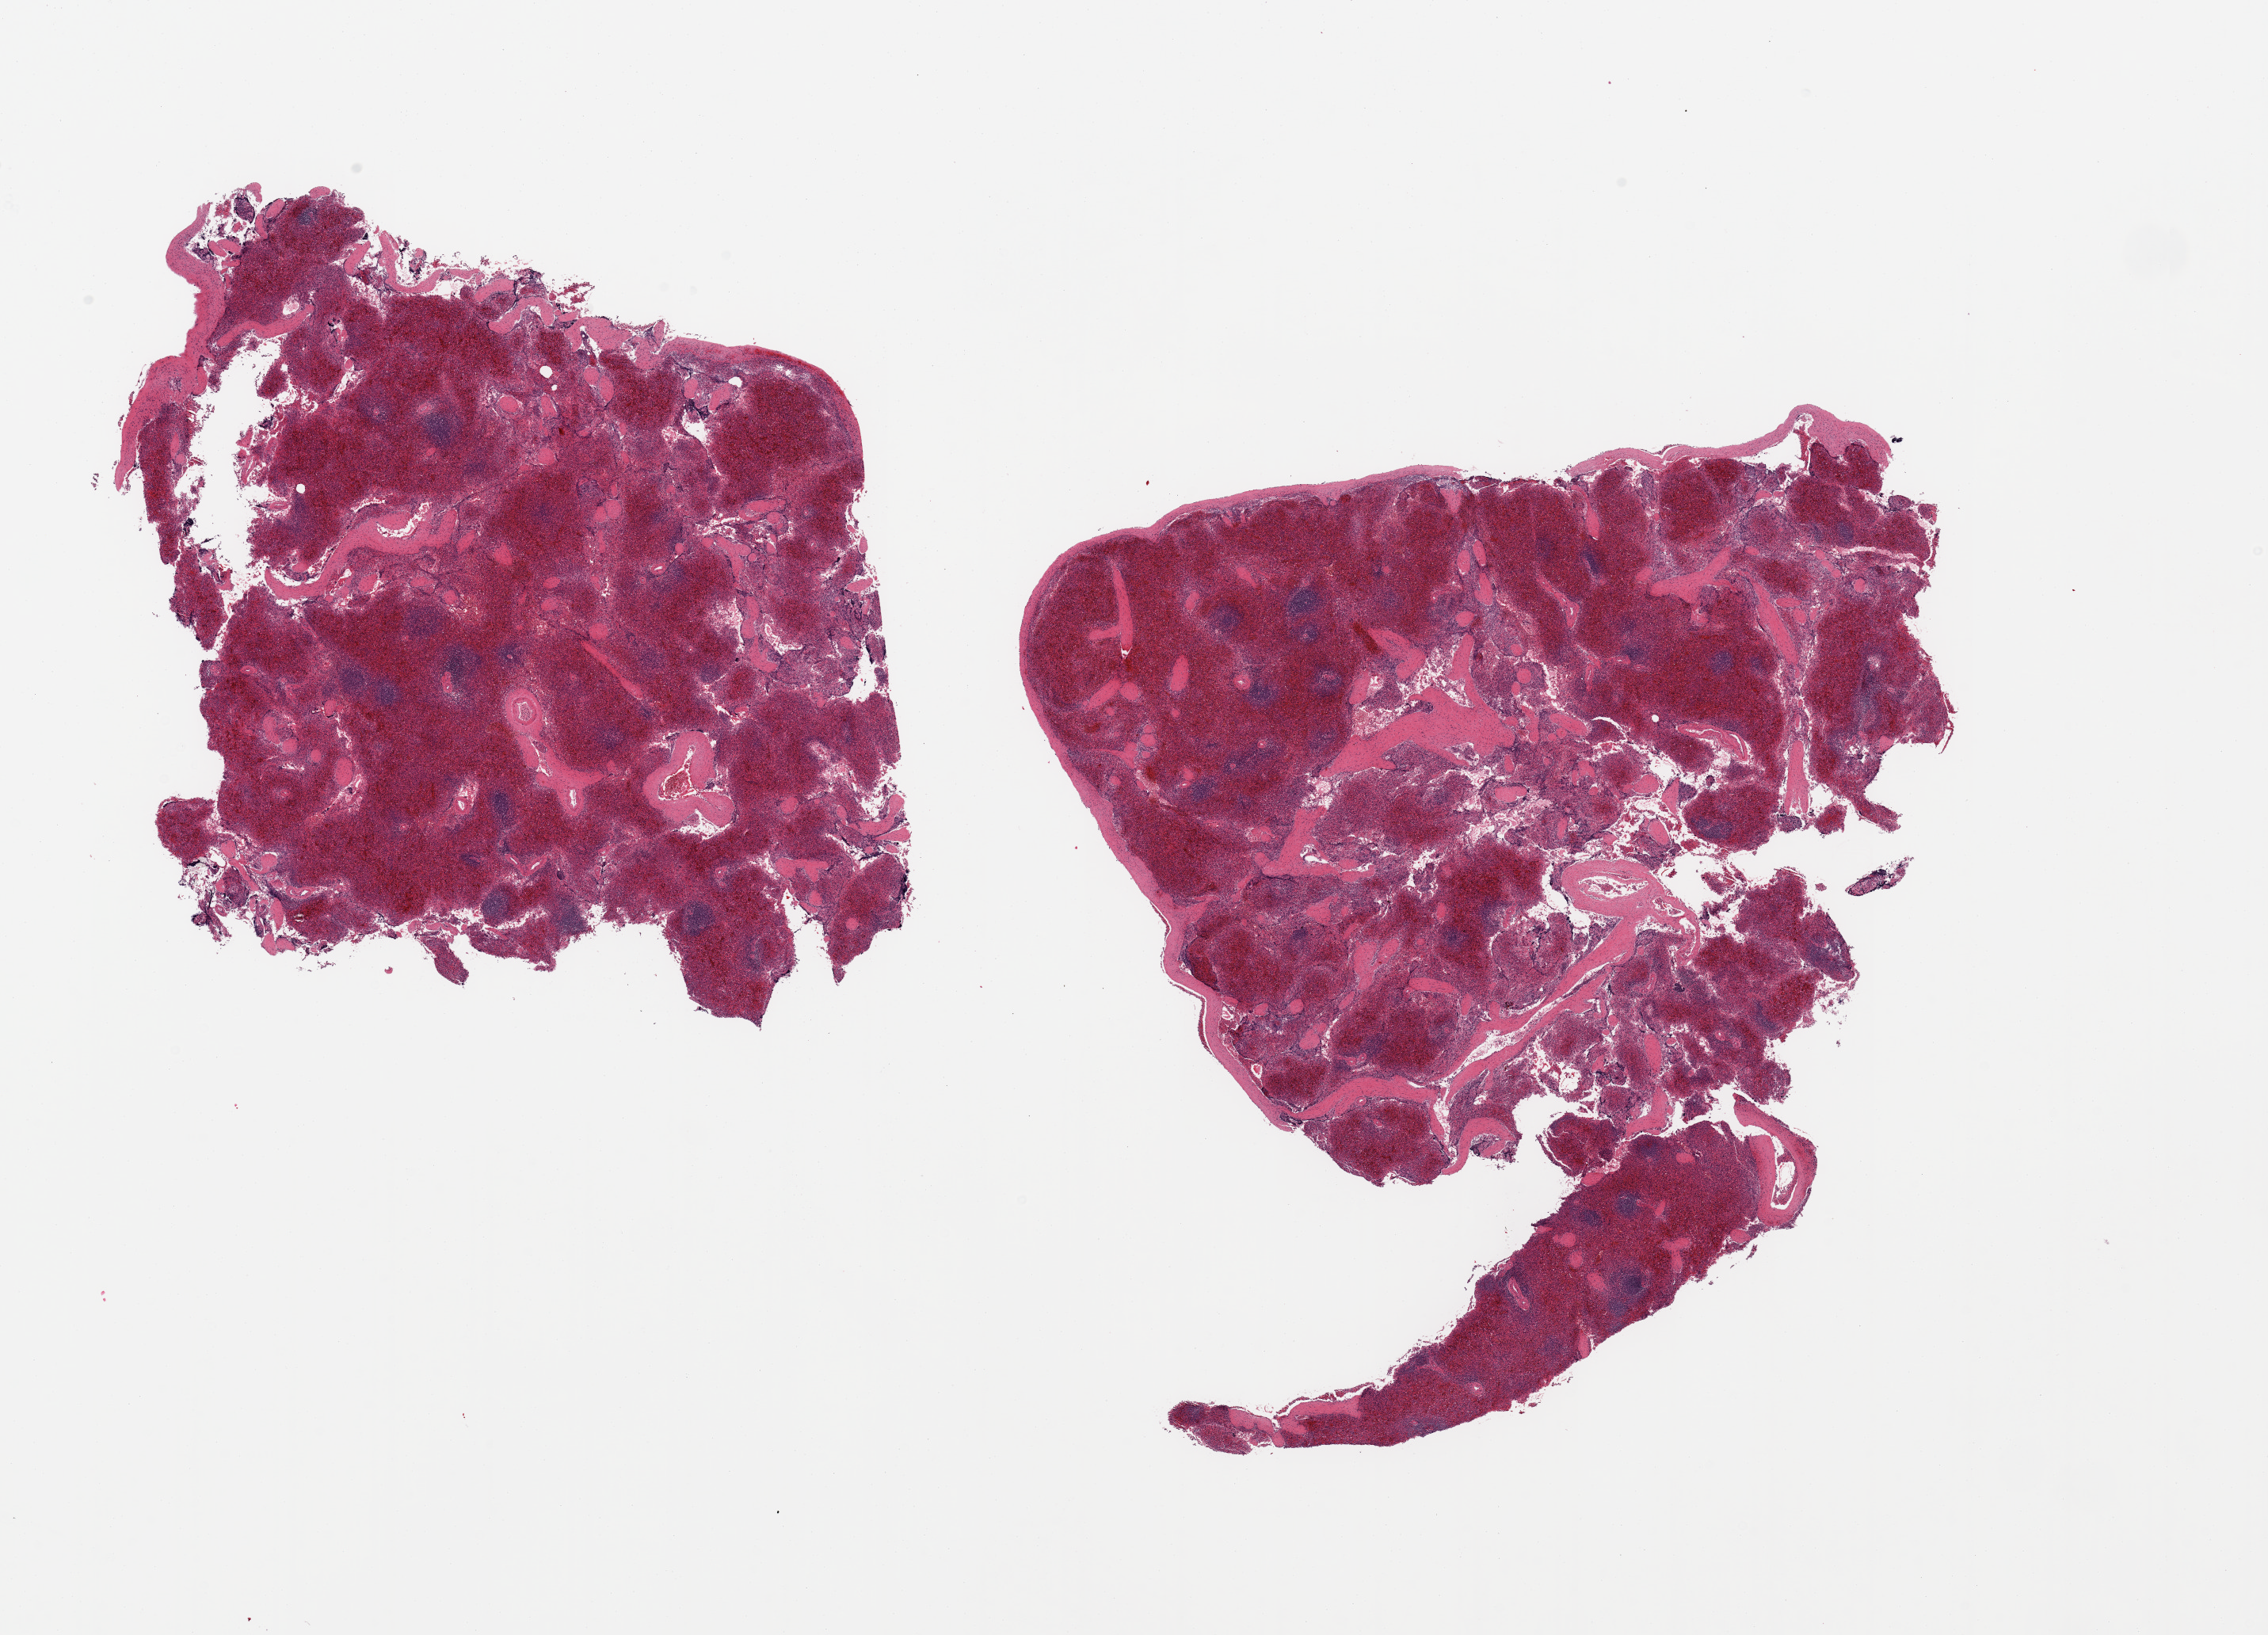
Digitized H&E-stained section, brightfield — whole scanned area (about 22.6 x 16.3 mm) shown as a low-resolution overview. PAXgene-fixed, paraffin-embedded tissue. Sampled site (target tissue): spleen. Donor tissue sample. Donor: male.
Pathologist's review note for this sample: 2 fragmented pieces; moderate congestion.